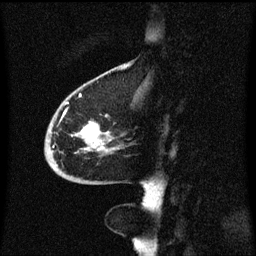
Breast MRI (dynamic contrast-enhanced), one sagittal slice. Position 20 of 60 along the scan axis. Dynamic contrast-enhanced series, image 2 of 3 at this slice position (ordered by acquisition). 1.5 T. TE 4.2 ms, TR 8.4 ms. 256 × 256 image matrix, field of view 200 × 200 mm. Patient: female, 68 years. Case-level facts recorded for this patient, not image findings: setting: breast cancer imaged before/during neoadjuvant chemotherapy; receptor status: triple-negative.
Outlined on this slice (semi-automatic segmentation, software-assisted and operator-edited):
- analysis volume of interest (the breast-tissue region the enhancement analysis was run in; not a lesion): bounding box (x1, y1, x2, y2) in pixels: (46, 94, 126, 173)
- tumour enhancement mask (voxels above the 70 % enhancement threshold inside the analysis volume of interest): (54, 94, 110, 167)